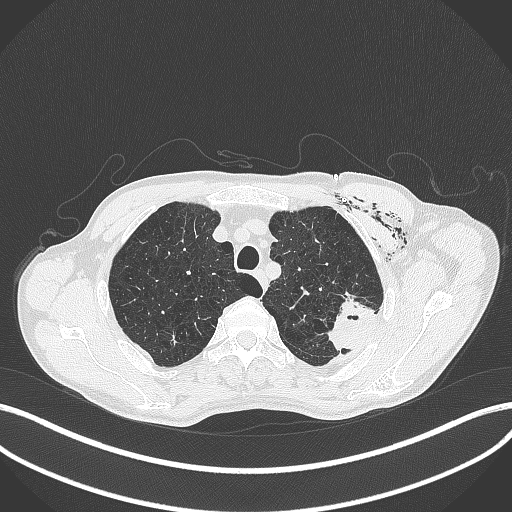
Chest CT, one axial slice; position 339 of 457 along the scan axis; reconstruction kernel B70f; 120 kVp; lung window (W 1500 / L -600 HU); 1 mm slice thickness; 512 × 512 image matrix, field of view 400 × 400 mm. Patient: male, 58 years. From the clinical record (not read from this slice): clinical TNM (as recorded): T3 N0 M0.
Annotated regions visible in this slice (rectangle marked by the reading radiologist):
- lung tumour (recorded histology: adenocarcinoma): bounding box <320,293,380,352> (left, top, right, bottom; pixels)